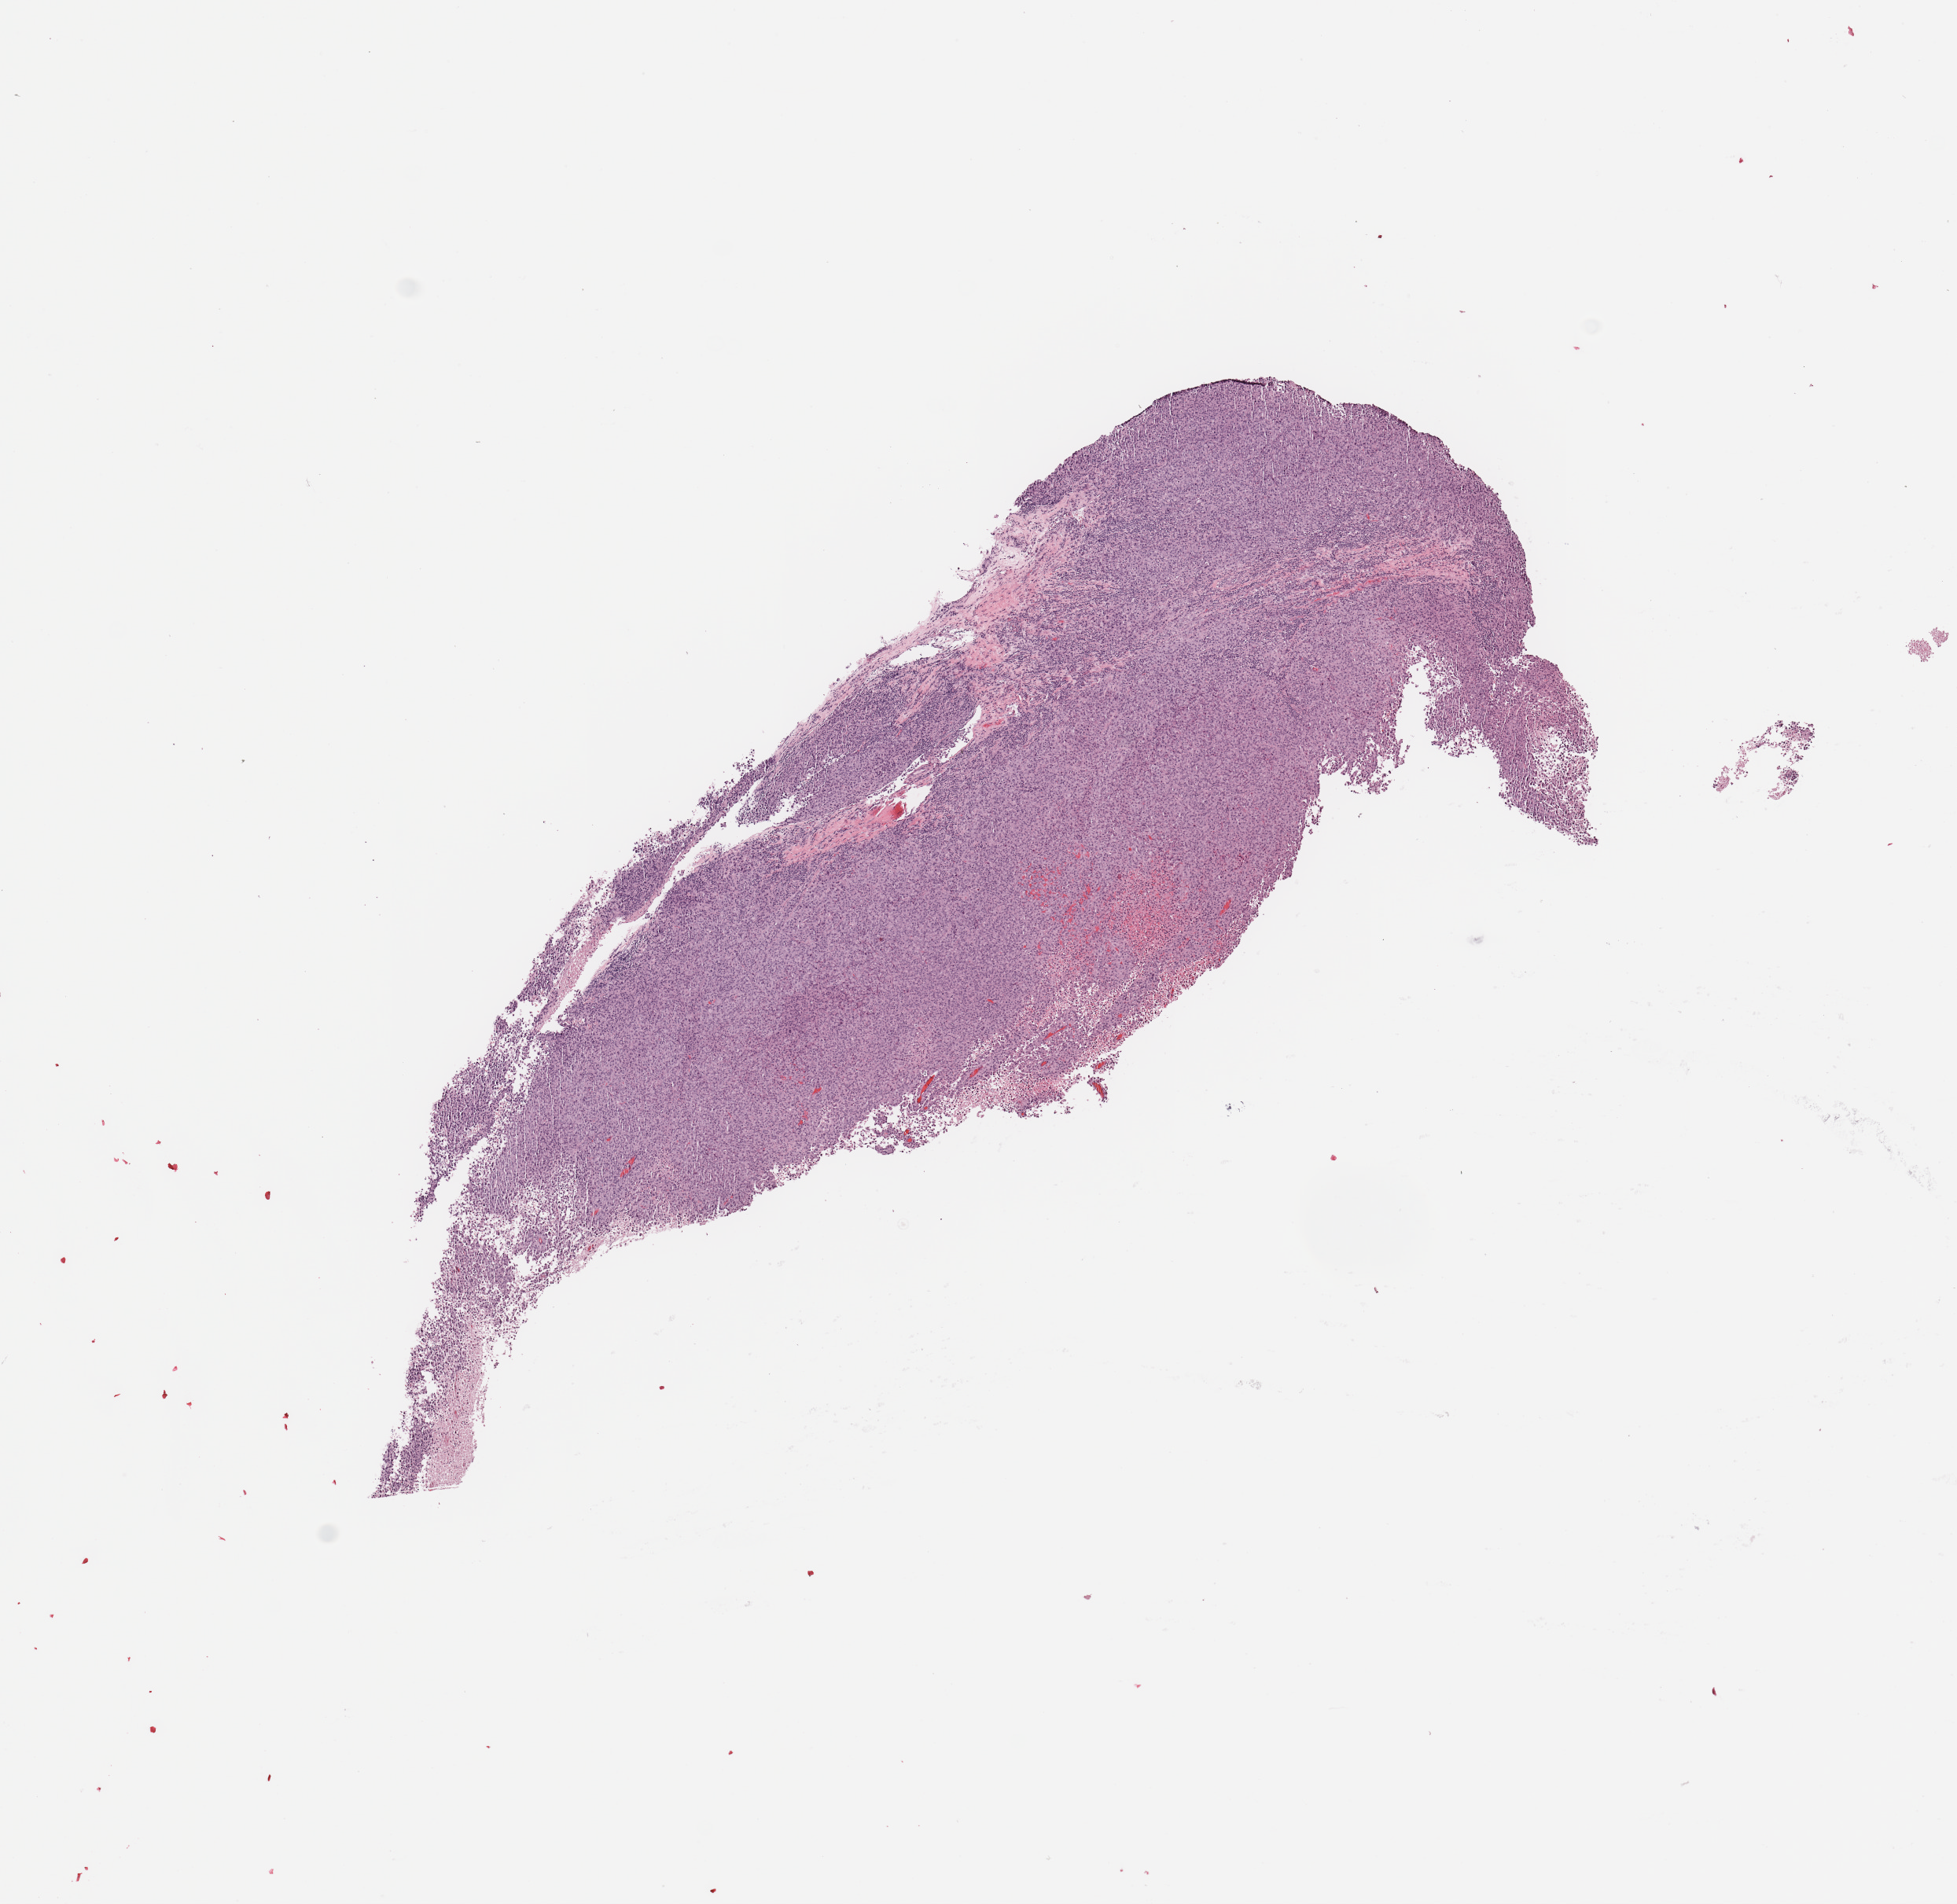
H&E whole-slide image — a low-resolution overview of the entire scanned area, about 9.8 x 9.6 mm (acquisition: 20x scan); tumour tissue sample. Male, 78 y/o.
* patient diagnosis (cohort enrolment): sarcoma (site not recorded at cohort level)
* primary tumour site (as recorded): chest